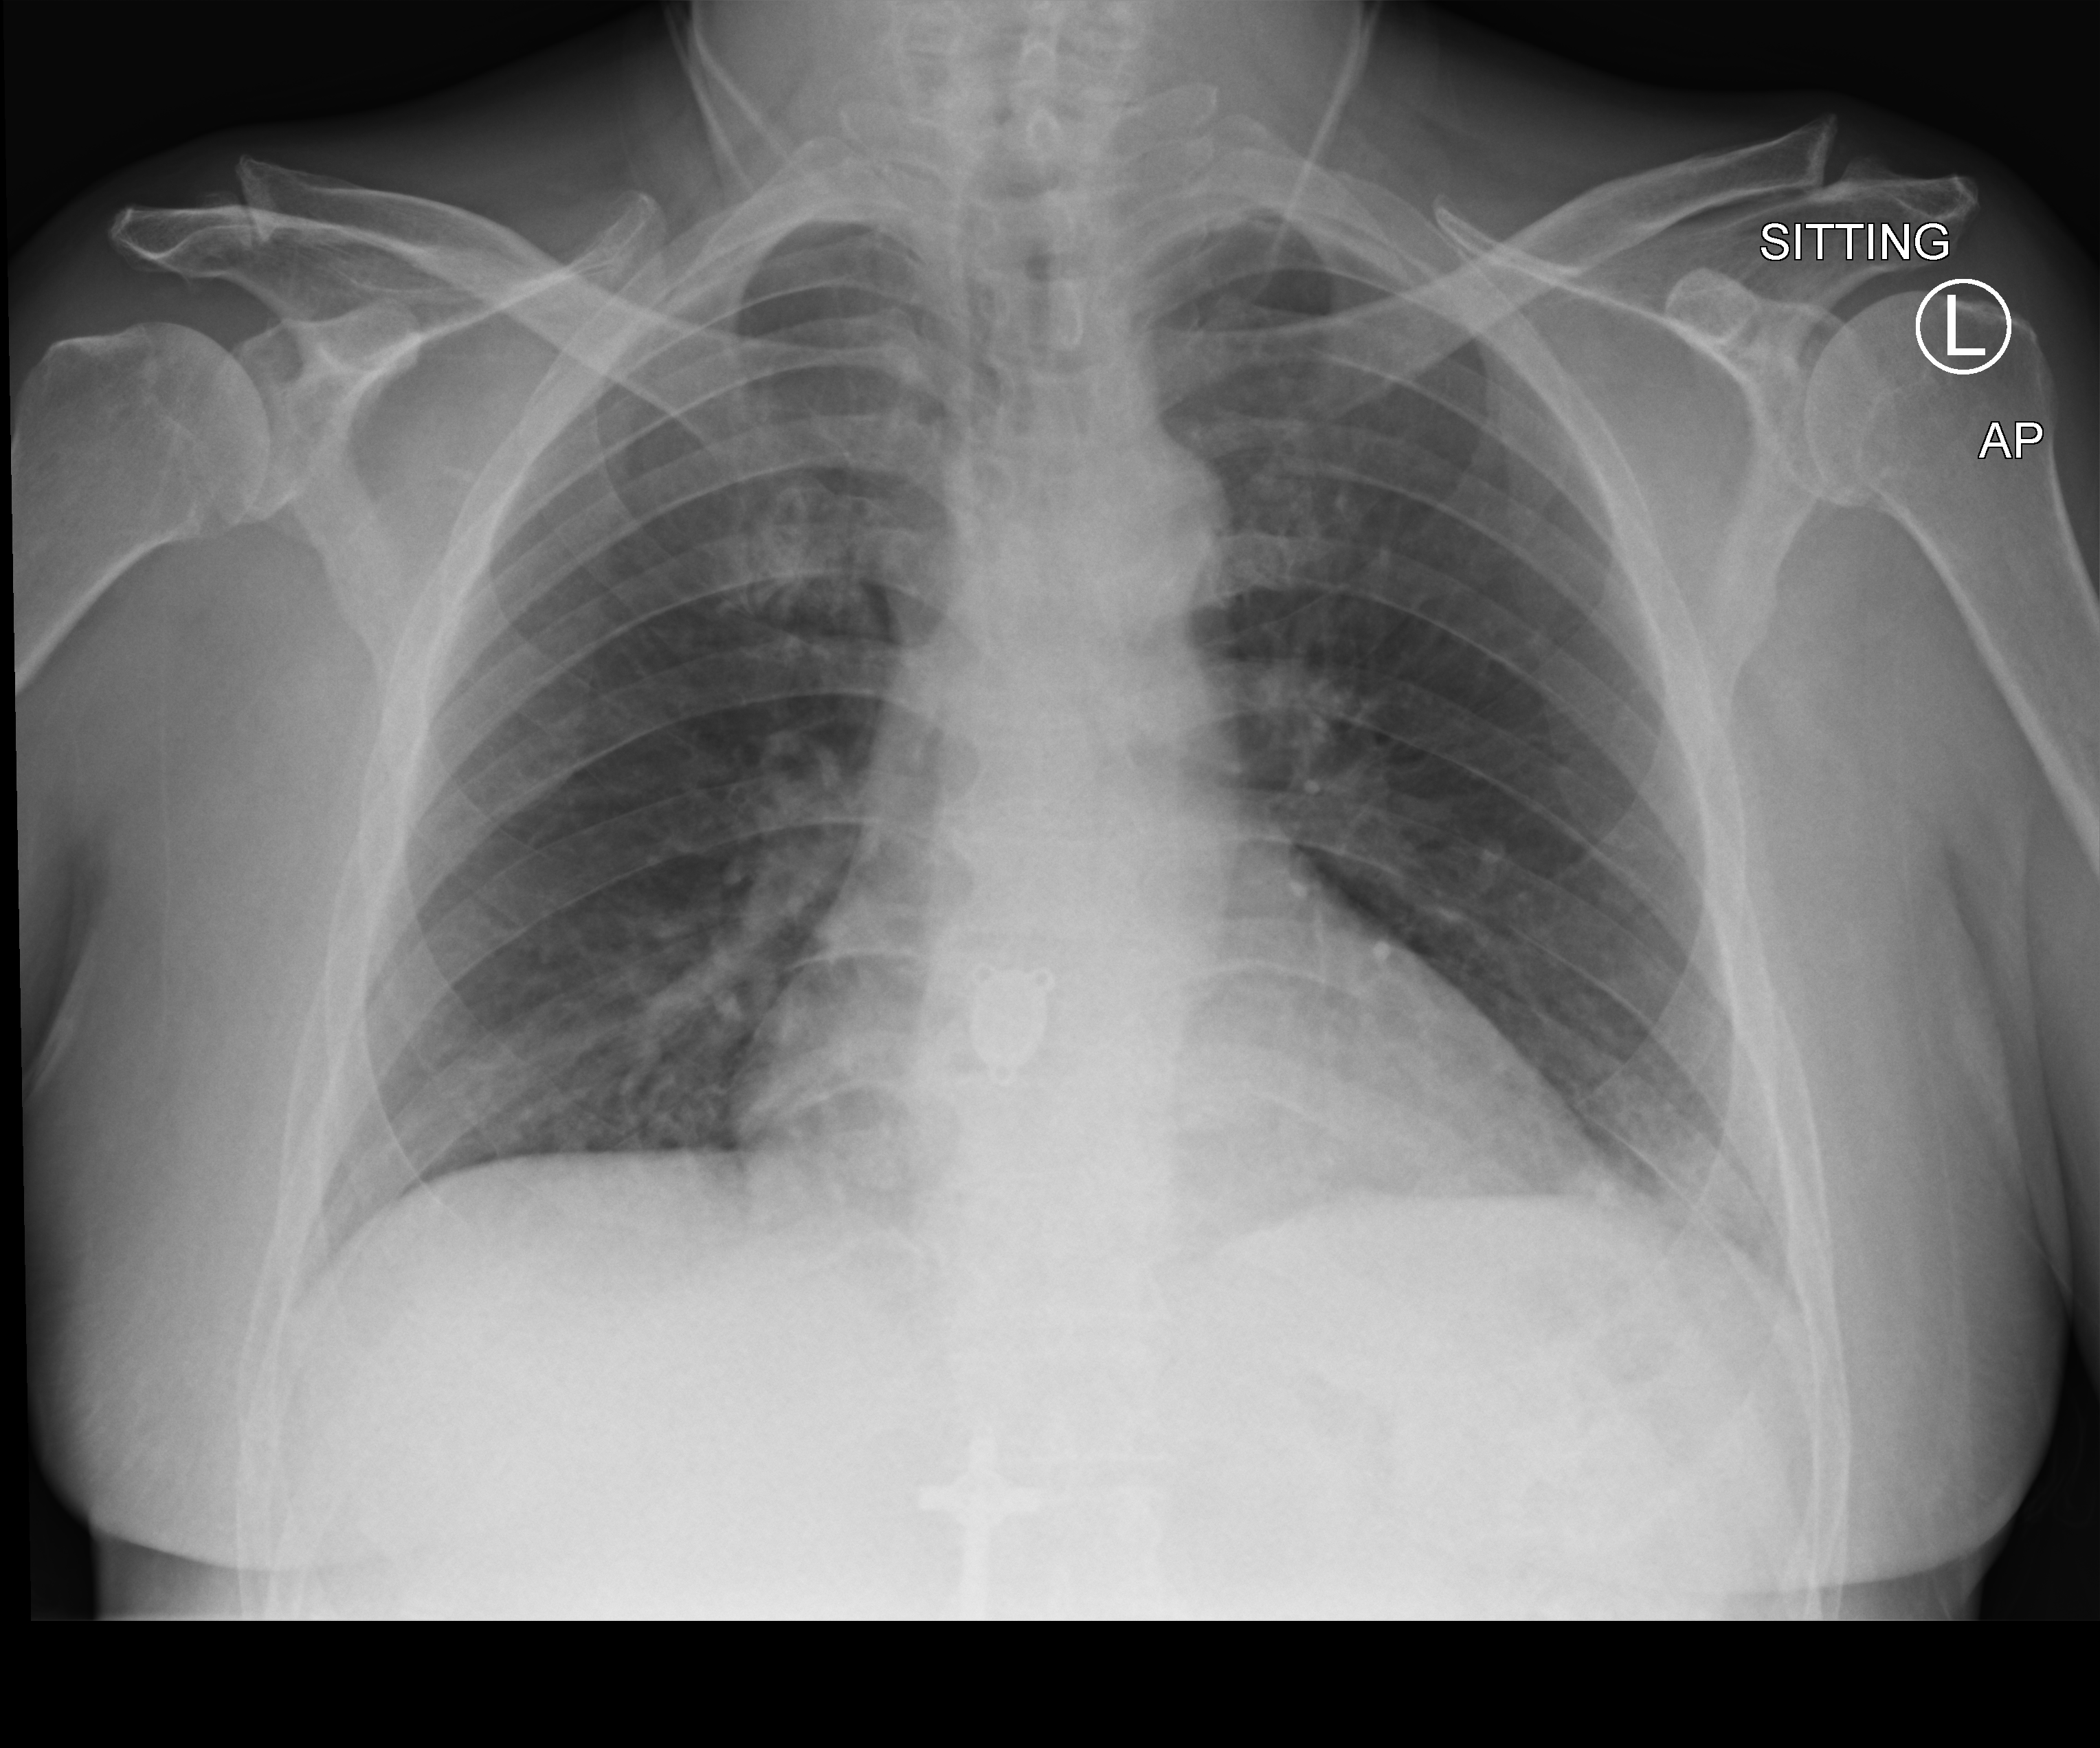
Portable chest radiograph; anteroposterior (AP) projection. Patient hospitalised with COVID-19; male, aged 18–59 years.
Admission-level facts for this patient (not findings on this image; timing relative to this image not recorded): mechanically ventilated during this hospital stay: no.